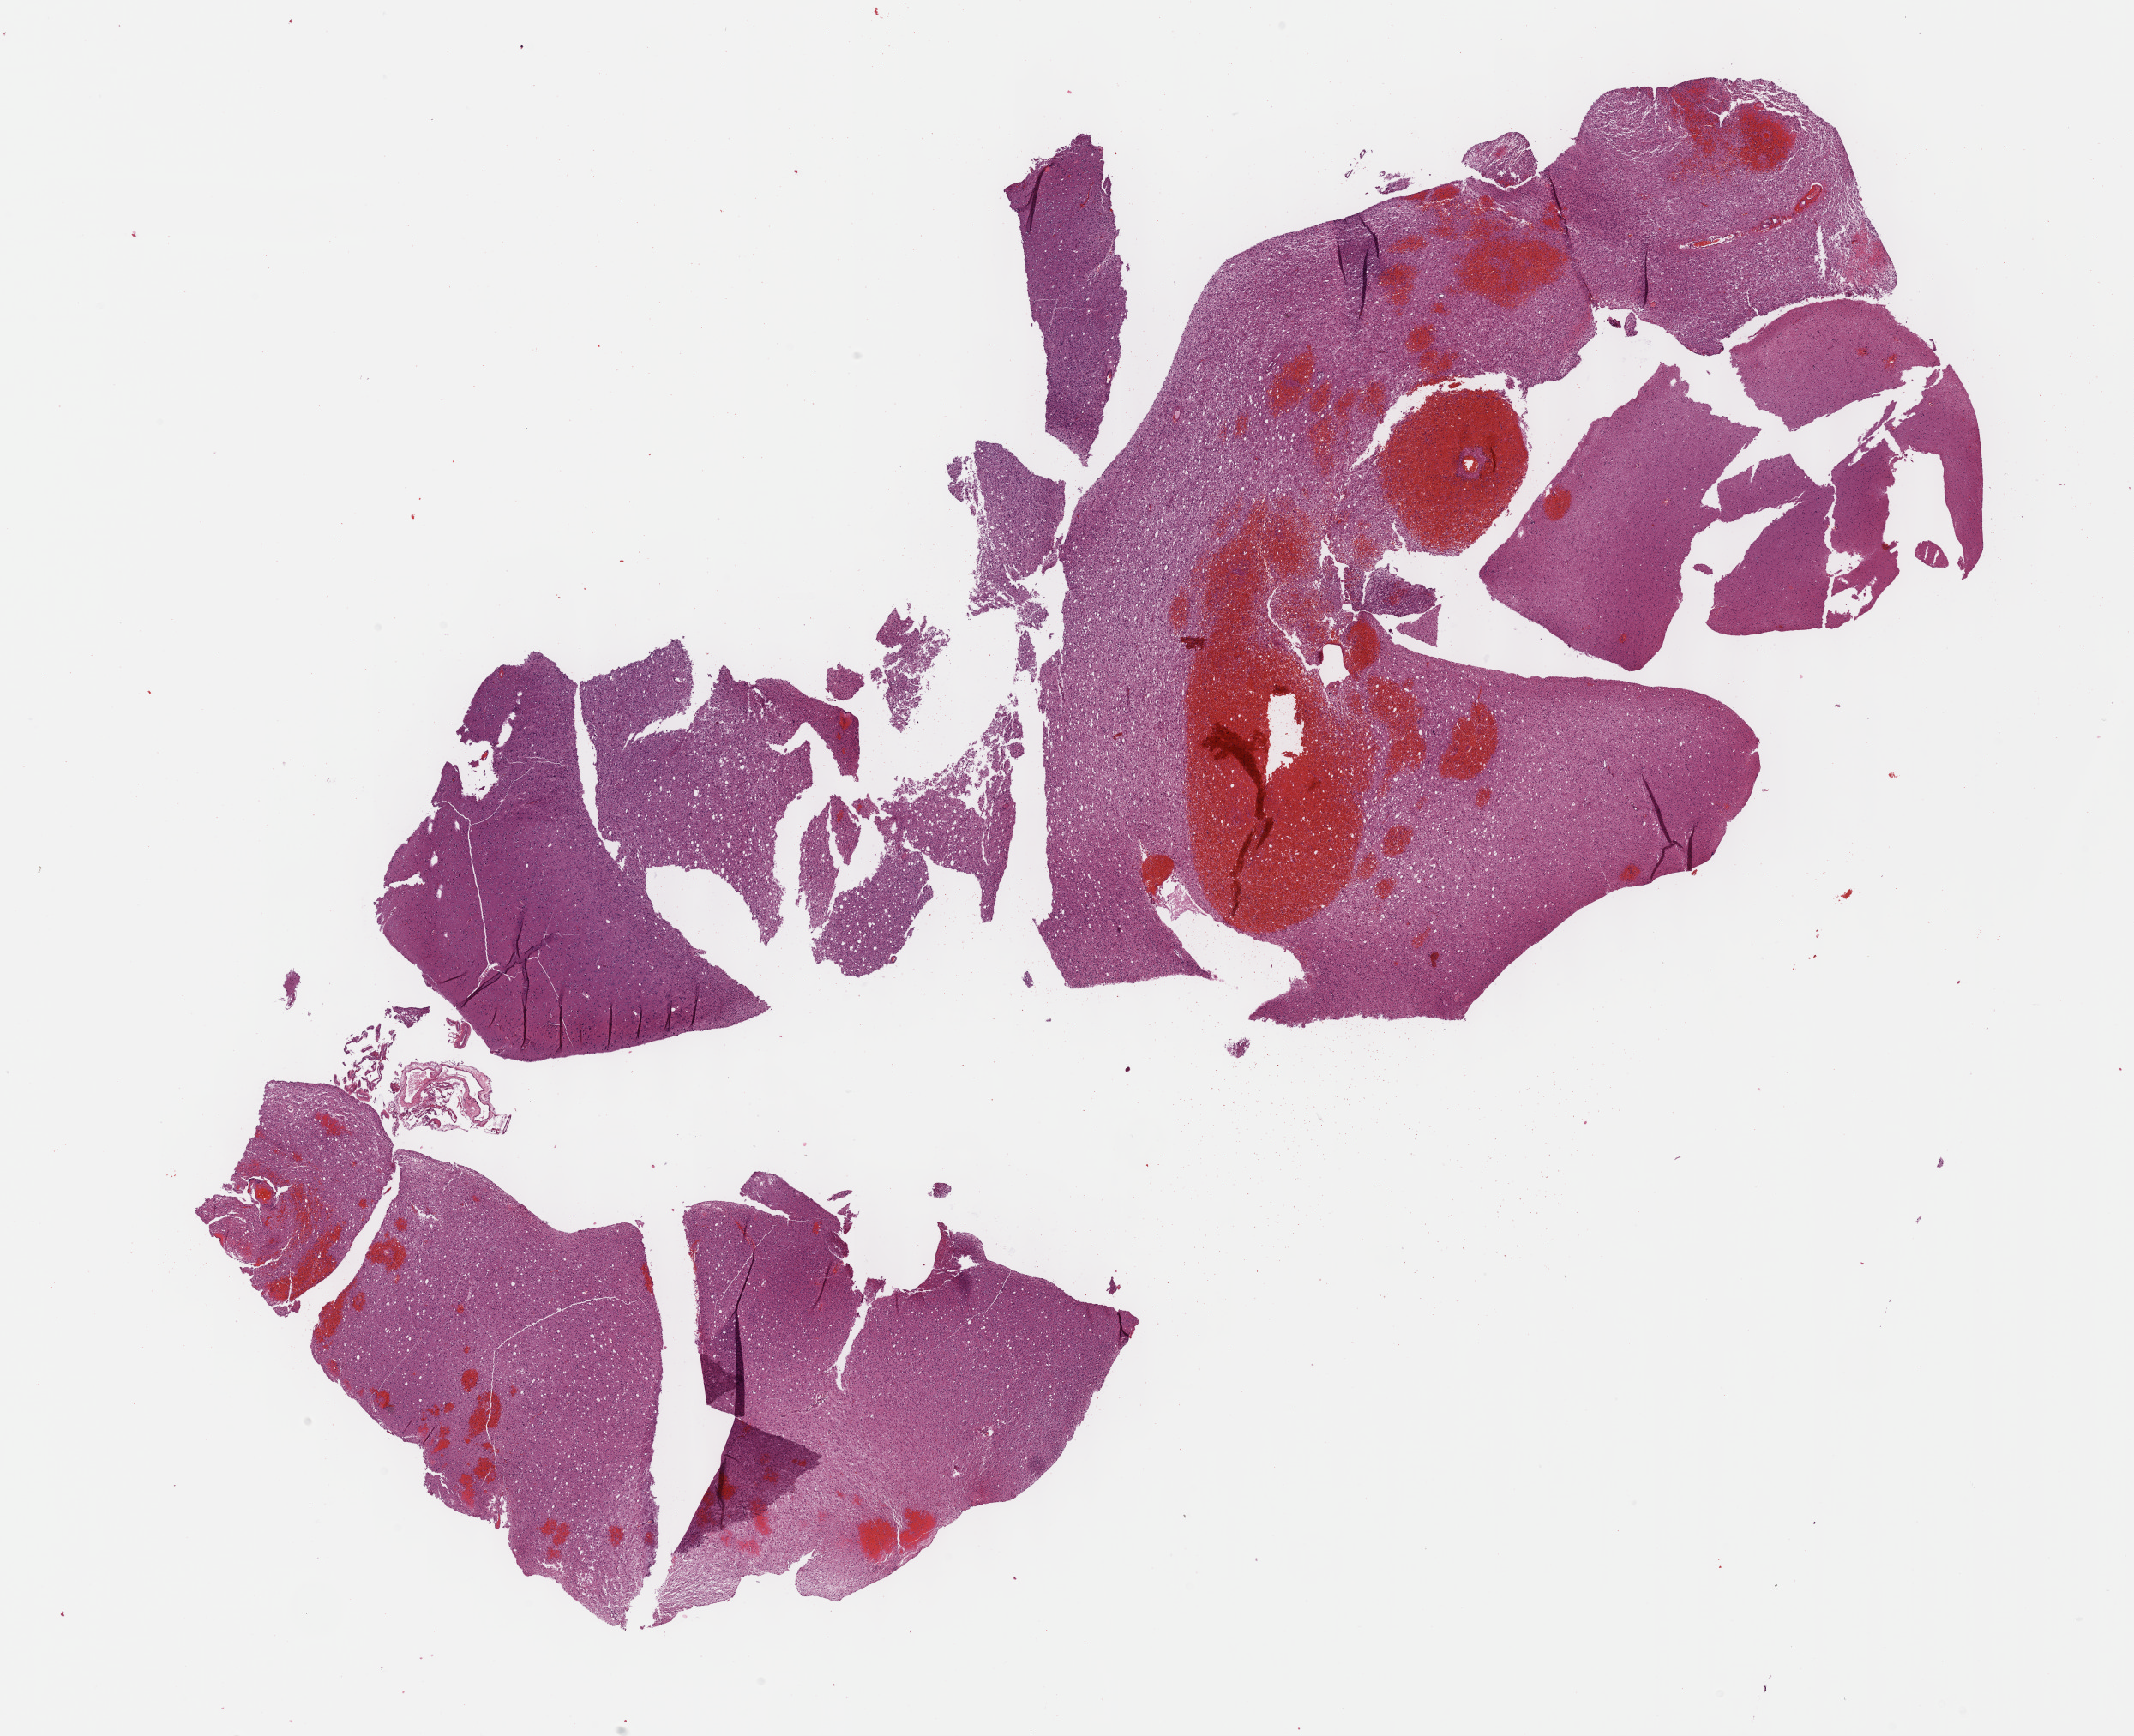
Digitized Hematoxylin and eosin (H&E) stained tissue section (whole slide), whole scanned area (about 20.1 x 16.4 mm, acquisition: 40x scan) shown as a low-resolution overview. Formalin-fixed paraffin-embedded (FFPE) diagnostic section. Brain, primary tumour sample. Female, age 29 years at initial diagnosis. Histologic grade: G2 (moderately differentiated).
• histologic diagnosis: Mixed glioma (cerebrum)